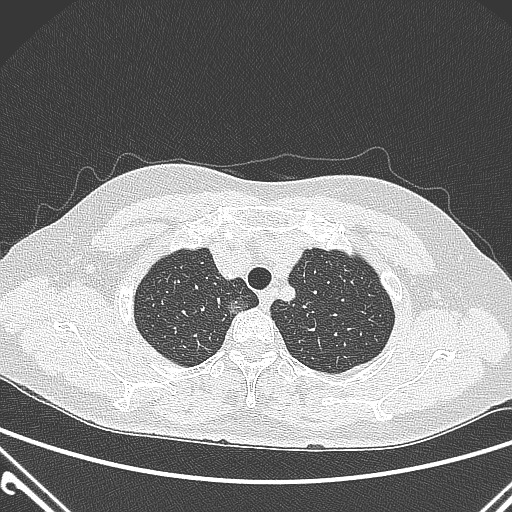
Chest CT, one axial slice. 120 kVp. Lung window (W 1500 / L -600 HU). 1 mm slice thickness. 512 × 512 image matrix, field of view 350 × 350 mm. Patient: female, 54 years. From the clinical record (not read from this slice): clinical TNM (as recorded): T1a N0 M0.
Structures marked on this image (bounding box drawn by a radiologist):
- lung tumour (recorded histology: adenocarcinoma): box from (x=224, y=295) to (x=253, y=327) px